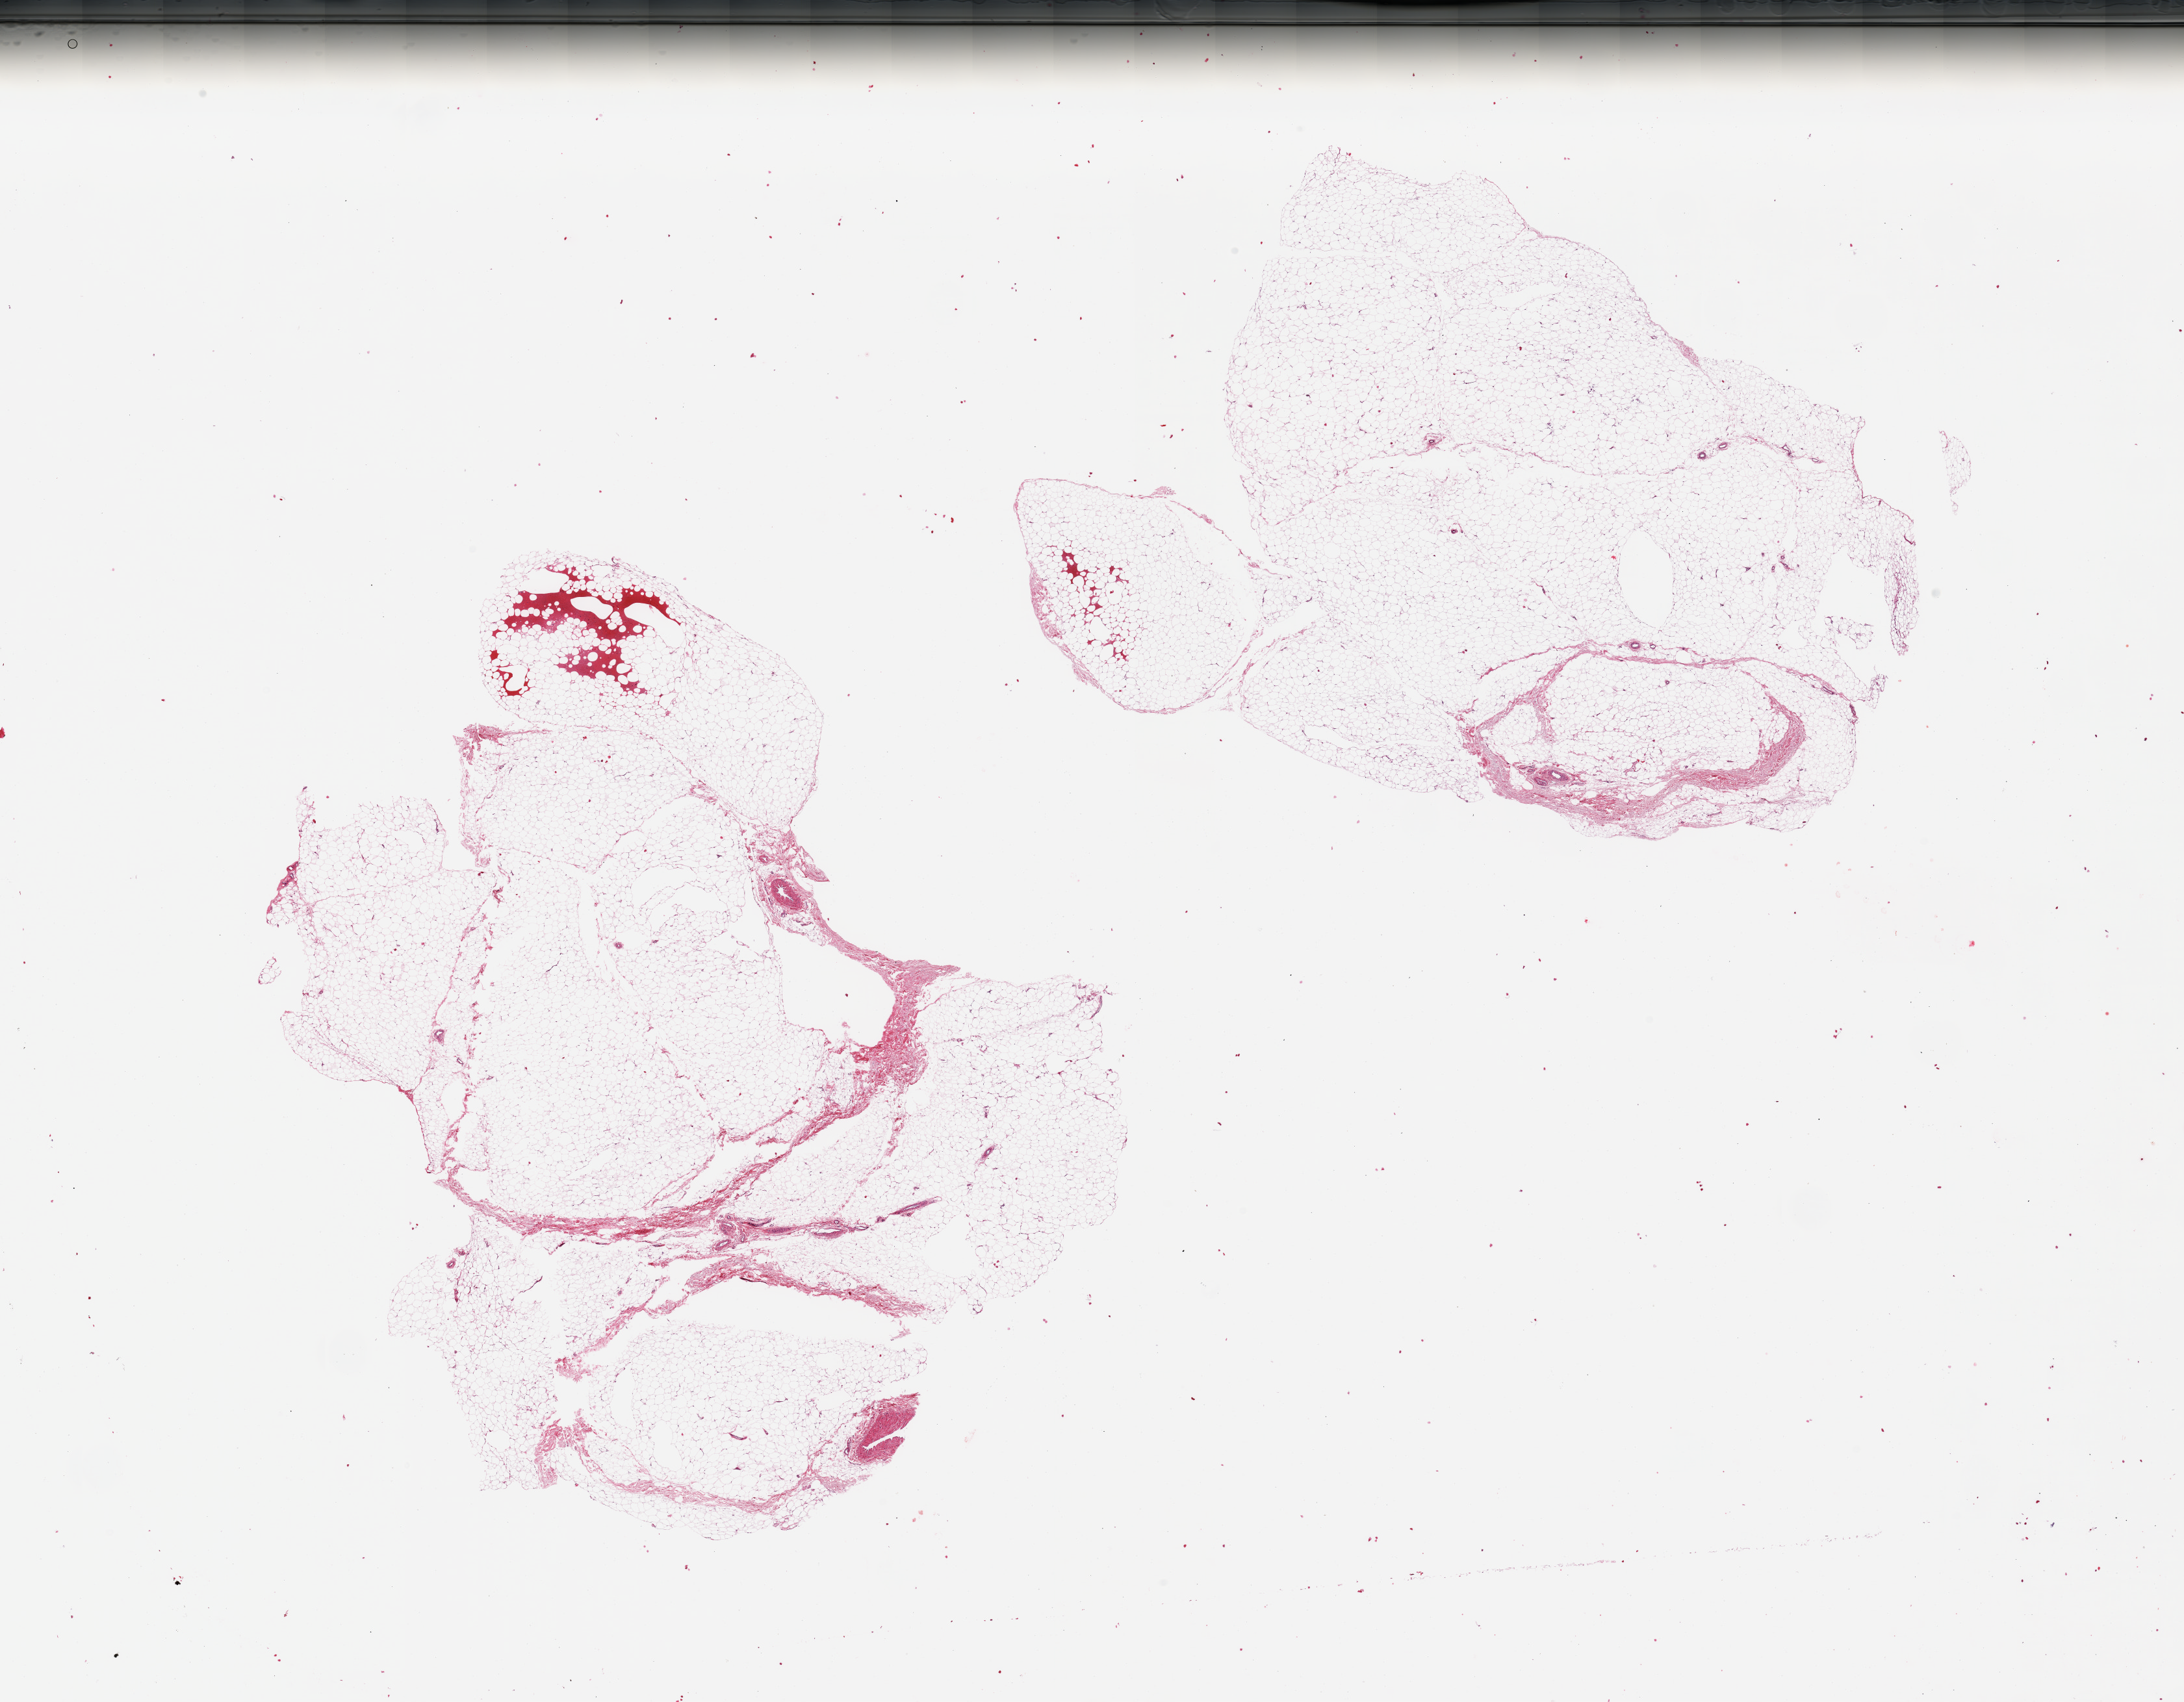
Whole-slide image, hematoxylin and eosin (H&E) stain, brightfield, a low-resolution overview of the entire scanned area, about 26.6 x 20.7 mm, PAXgene-fixed, paraffin-embedded tissue, section of adipose tissue (target tissue), donor tissue sample. Donor: male.
* review note (as recorded): 2 pieces; <2% fibrous stroma